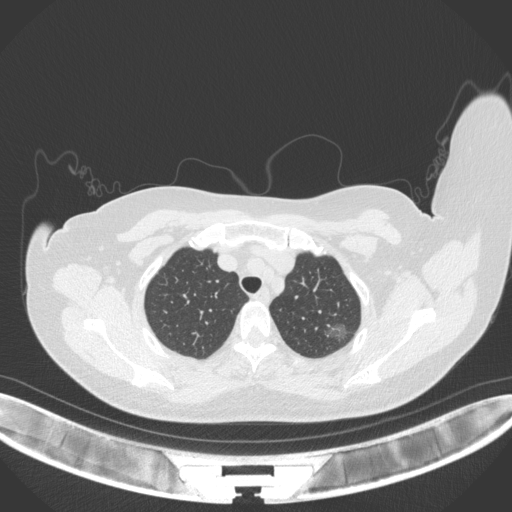
Chest CT, one axial slice; position 307 of 386 along the scan axis; reconstruction kernel B31f; 120 kVp; lung window (W 1500 / L -600 HU); 512 × 512 image matrix. Patient: female, 58 years. From the clinical record (not read from this slice): clinical TNM (as recorded): T1c N0 M0.
Structures marked on this image (bounding box drawn by a radiologist):
- lung tumour (recorded histology: adenocarcinoma): bounding box <320,320,357,346> (left, top, right, bottom; pixels)